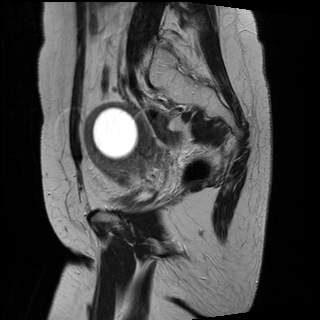
Pelvic MRI for cervical cancer, one sagittal slice. Position 22 of 29 along the scan axis. T2-weighted. 1.5 T. TE 89 ms, TR 2930 ms. 4 mm slice thickness. 320 × 320 image matrix, field of view 260 × 260 mm. Patient: female, 49 years.
Outlined on this slice (outlined manually by an expert reader):
- uterus and cervix: box from (x=85, y=100) to (x=157, y=185) px